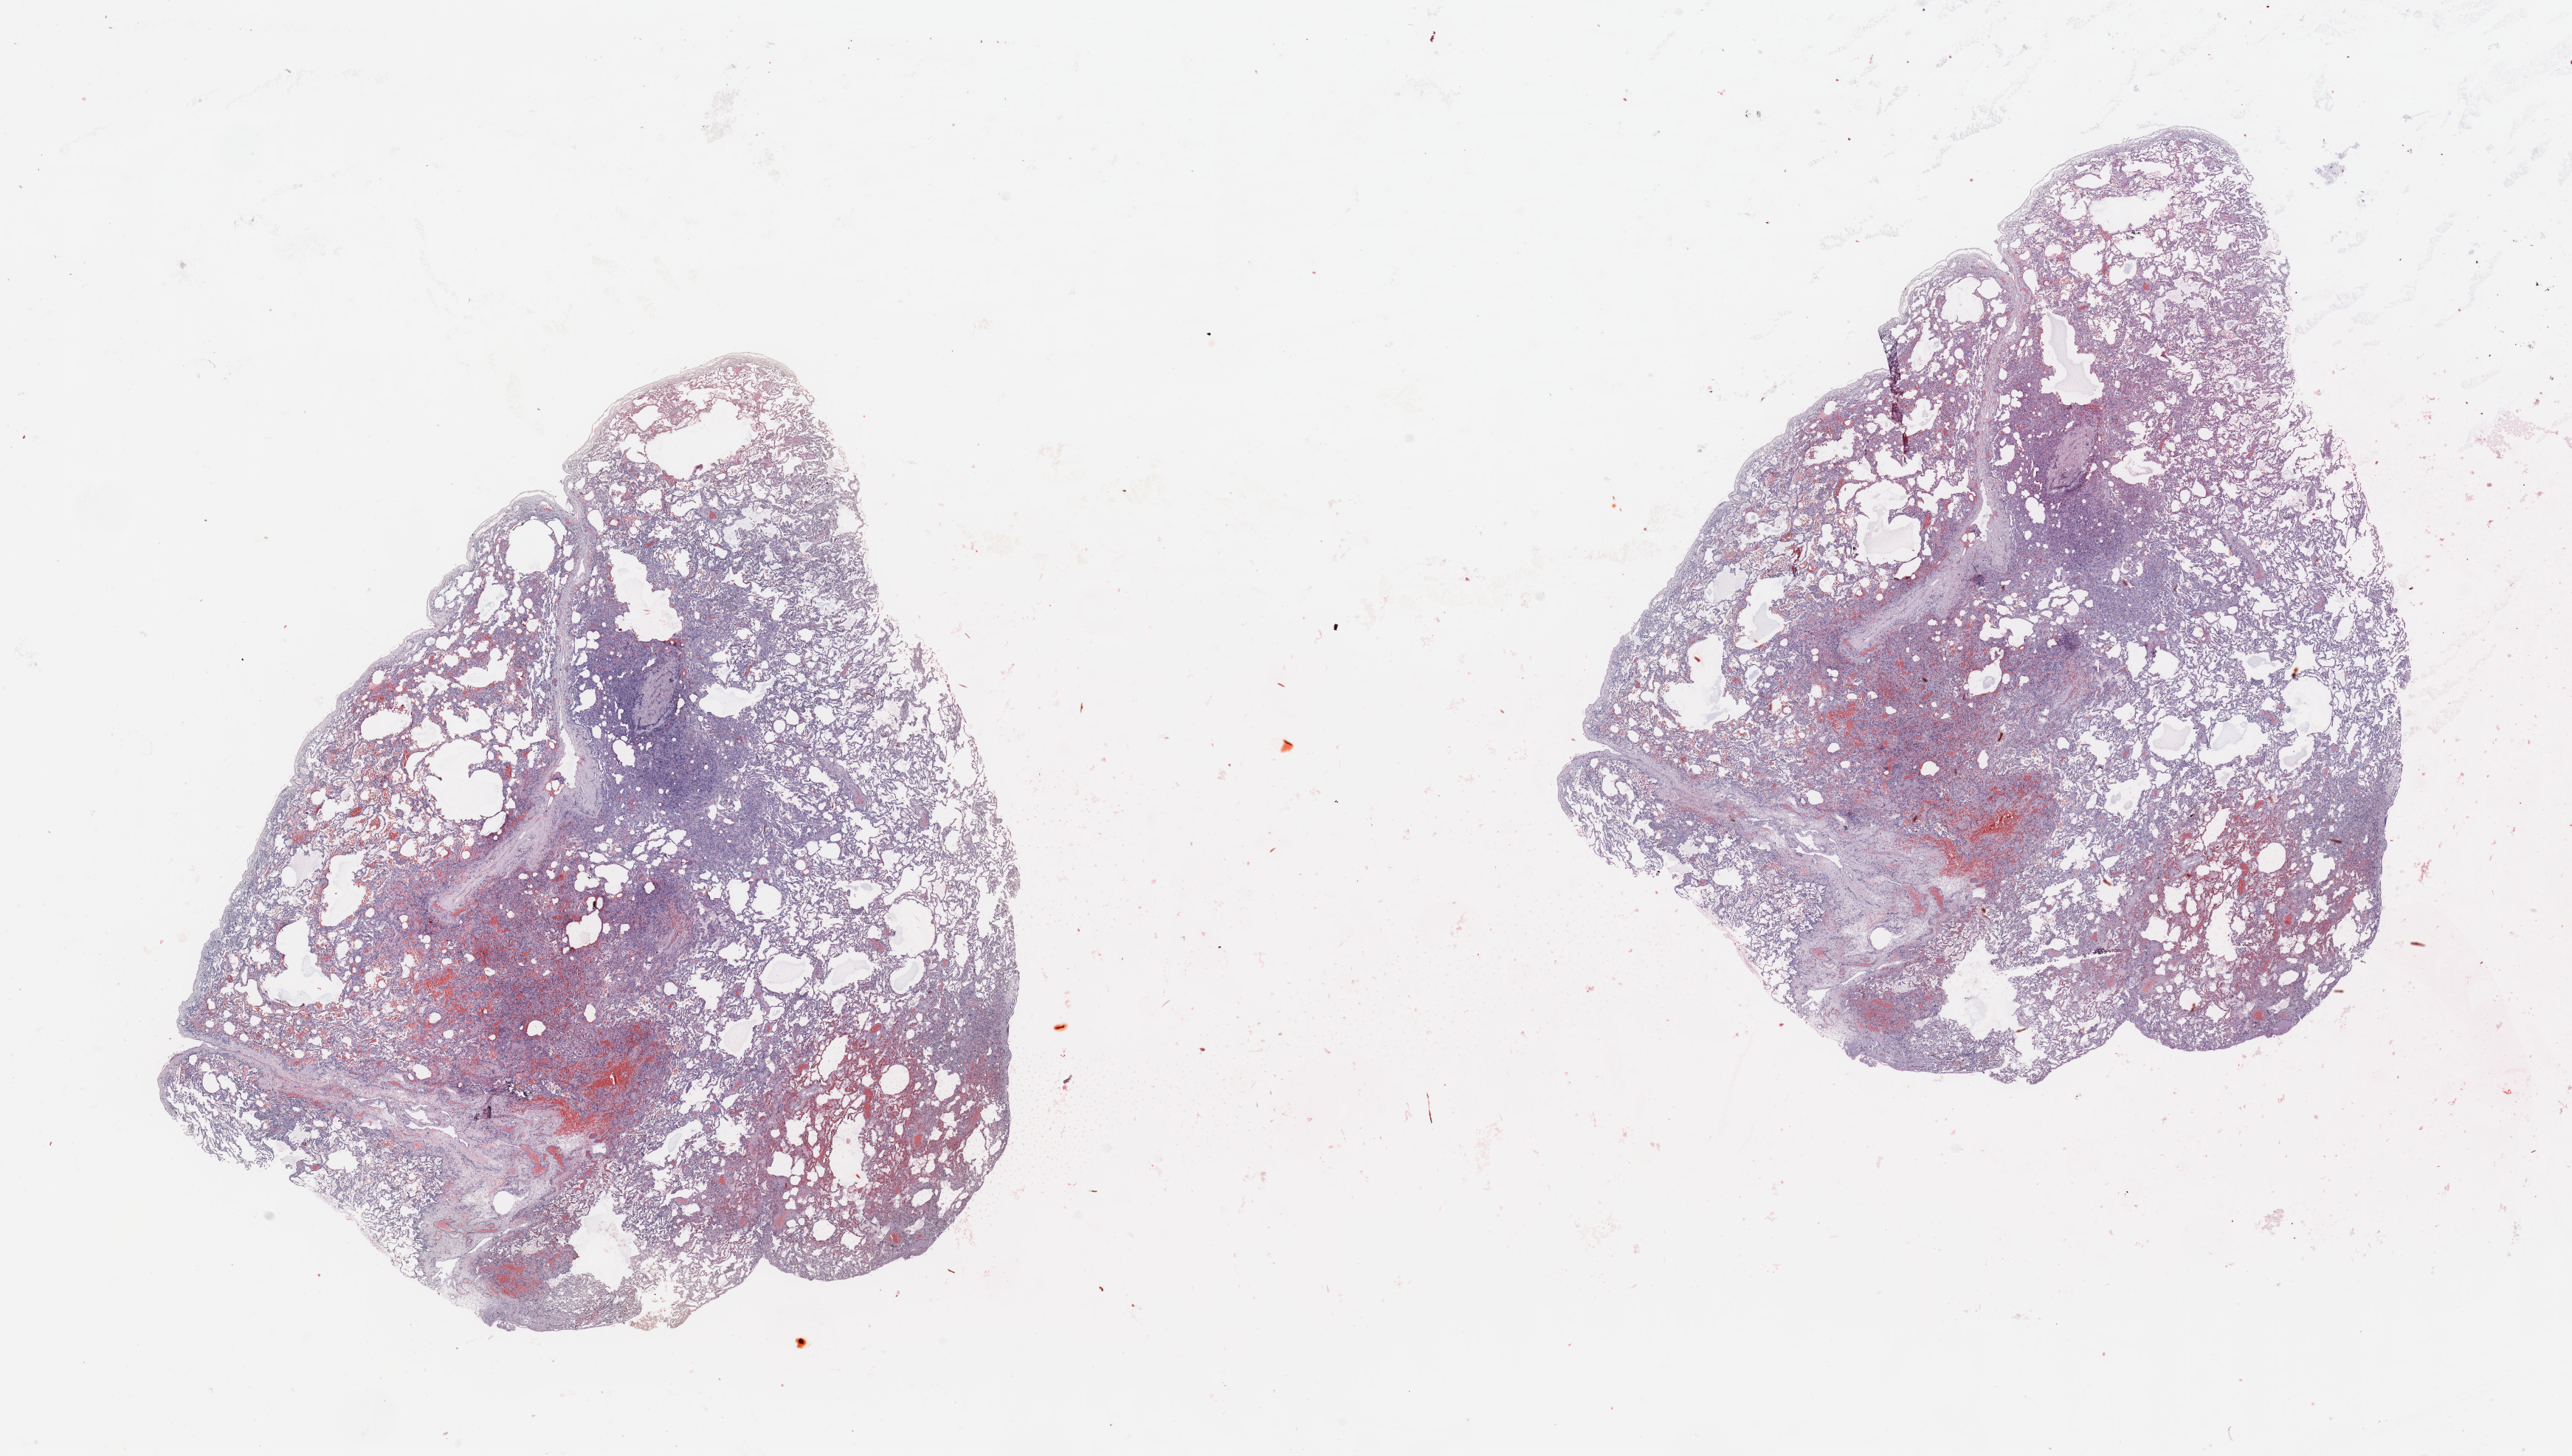
H&E whole-slide image — a low-resolution overview of the entire scanned area, about 27.6 x 15.6 mm; lung, normal (non-tumour) tissue. Female, 48 y/o.
This section: normal (non-tumour) tissue from the same patient. Patient diagnosis: Squamous cell carcinoma, NOS.